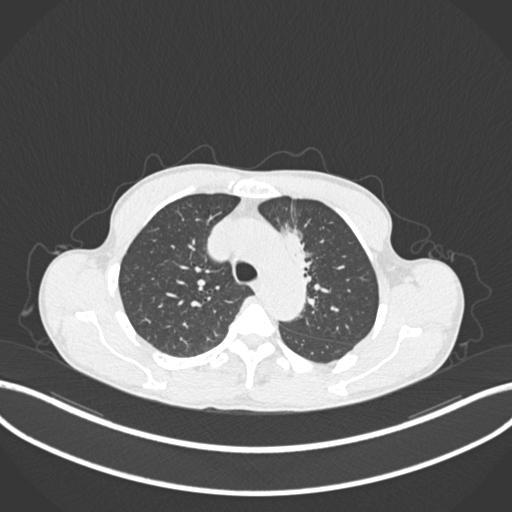
Chest CT, one axial slice. Slice 147 of 211 in the series (ordered by position). Reconstruction kernel B30f. Lung window (W 1500 / L -600 HU). 1 mm slice thickness. 512 × 512 image matrix, field of view 400 × 400 mm. Patient: male, 58 years. From the clinical record (not read from this slice): clinical TNM (as recorded): T1c N1 M0.
Structures marked on this image (bounding box drawn by a radiologist):
- lung tumour (recorded histology: adenocarcinoma): bounding box <278,213,313,280> (left, top, right, bottom; pixels)